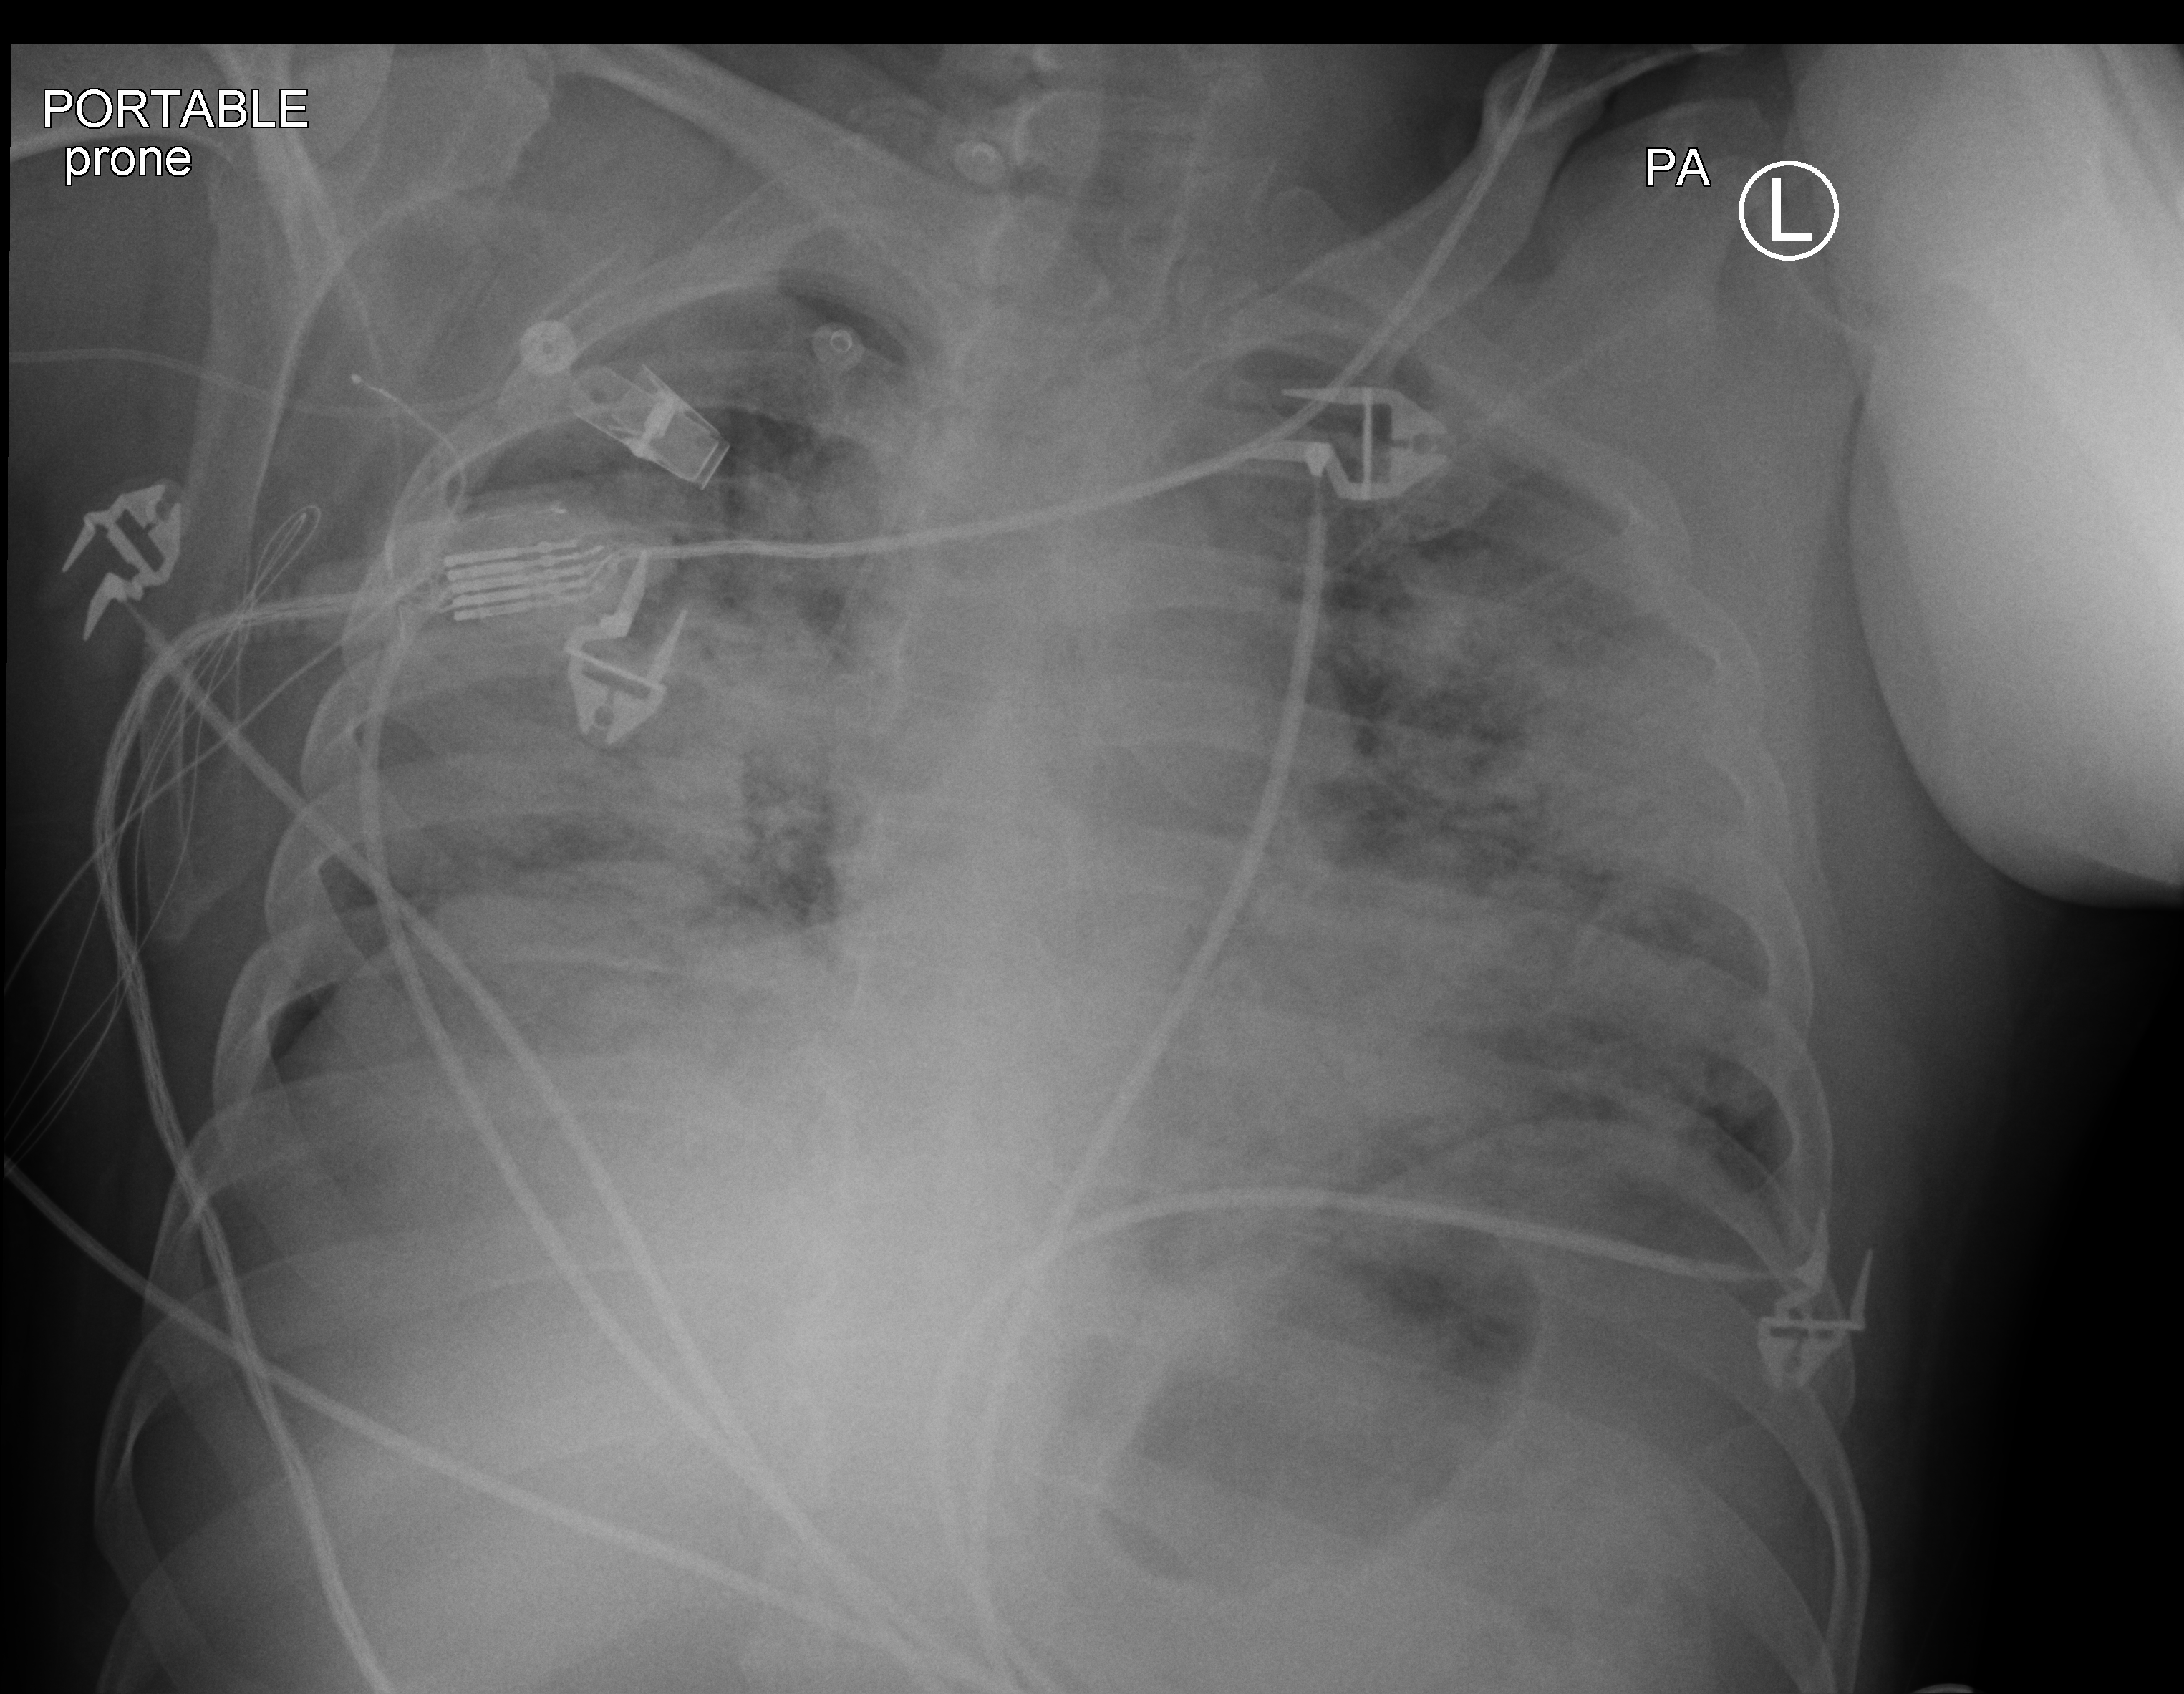
Portable chest radiograph; posteroanterior (PA) projection. Male patient hospitalised with COVID-19, age 18–59 years.
Hospital-stay facts (about this admission, not read from this image; timing relative to this image not recorded): admitted to intensive care during this hospital stay: yes; hypertension (admission record): no; mechanically ventilated during this hospital stay: yes.